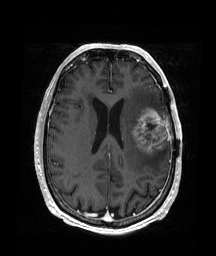
Brain MRI from a brain-tumour surgery series, one axial slice. Position 74 of 176 along the scan axis. T1-weighted post-contrast. 1 mm slice thickness. 216 × 256 image matrix, field of view 219 × 260 mm. Case-level facts recorded for this patient, not image findings: histopathology: Glioblastoma; WHO grade: 4; IDH mutation: no; tumour location: Left Frontal.
Outlined on this slice (expert manual segmentation):
- tumour: bounding box [x1, y1, x2, y2] px = [132, 108, 168, 155]